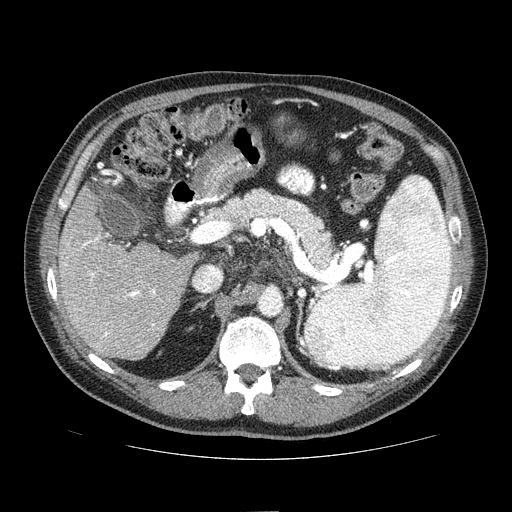
Contrast-enhanced abdominal CT (liver protocol), one axial slice. Slice 36 of 81 in the series (ordered by position). Reconstruction kernel STANDARD. One of 2 acquisitions stored at this slice position. Soft-tissue window (W 400 / L 40 HU). 512 × 512 image matrix, field of view 400 × 400 mm. Case-level facts recorded for this patient, not image findings: diagnosis: hepatocellular carcinoma (patient treated with transarterial chemoembolisation; whether this scan precedes or follows treatment is not stated here); TNM stage (as recorded): Stage-IIIA; Child-Pugh class: A; tumour differentiation: well differentiated; tumour nodularity: multinodular.
Structures marked on this image (semi-automatic segmentation, software-assisted and operator-edited):
- liver parenchyma outside the tumour (the mass and vessels are separate outlines, so this box may not span the whole liver): bounding box <58,179,198,360> (left, top, right, bottom; pixels)
- liver vessels: <64,237,156,340>